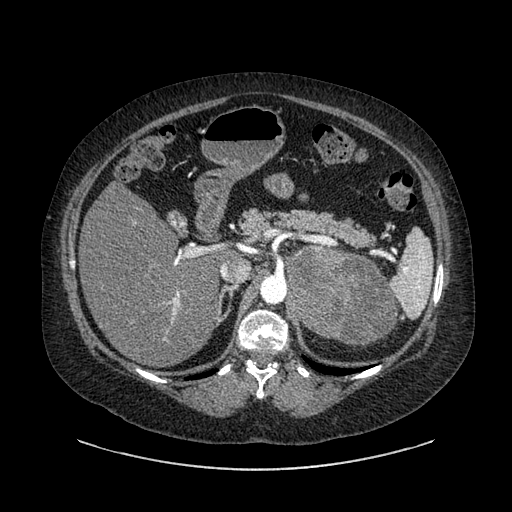
Contrast-enhanced abdominal CT, one axial slice. Reconstruction kernel SOFT. 120 kVp. Intravenous contrast given. Soft-tissue window (W 400 / L 40 HU). 0.62 mm slice thickness. 512 × 512 image matrix. Female patient, age 61 years. From the clinical record (not read from this slice): diagnosis: adrenocortical carcinoma; tumour side: left adrenal; tumour size at pathology: 13 cm; Ki-67 index: 79 %; stage (as recorded): 2.
Structures marked on this image (semi-automatically segmented with operator editing):
- mass: bounding box (x1, y1, x2, y2) in pixels: (287, 248, 395, 345)